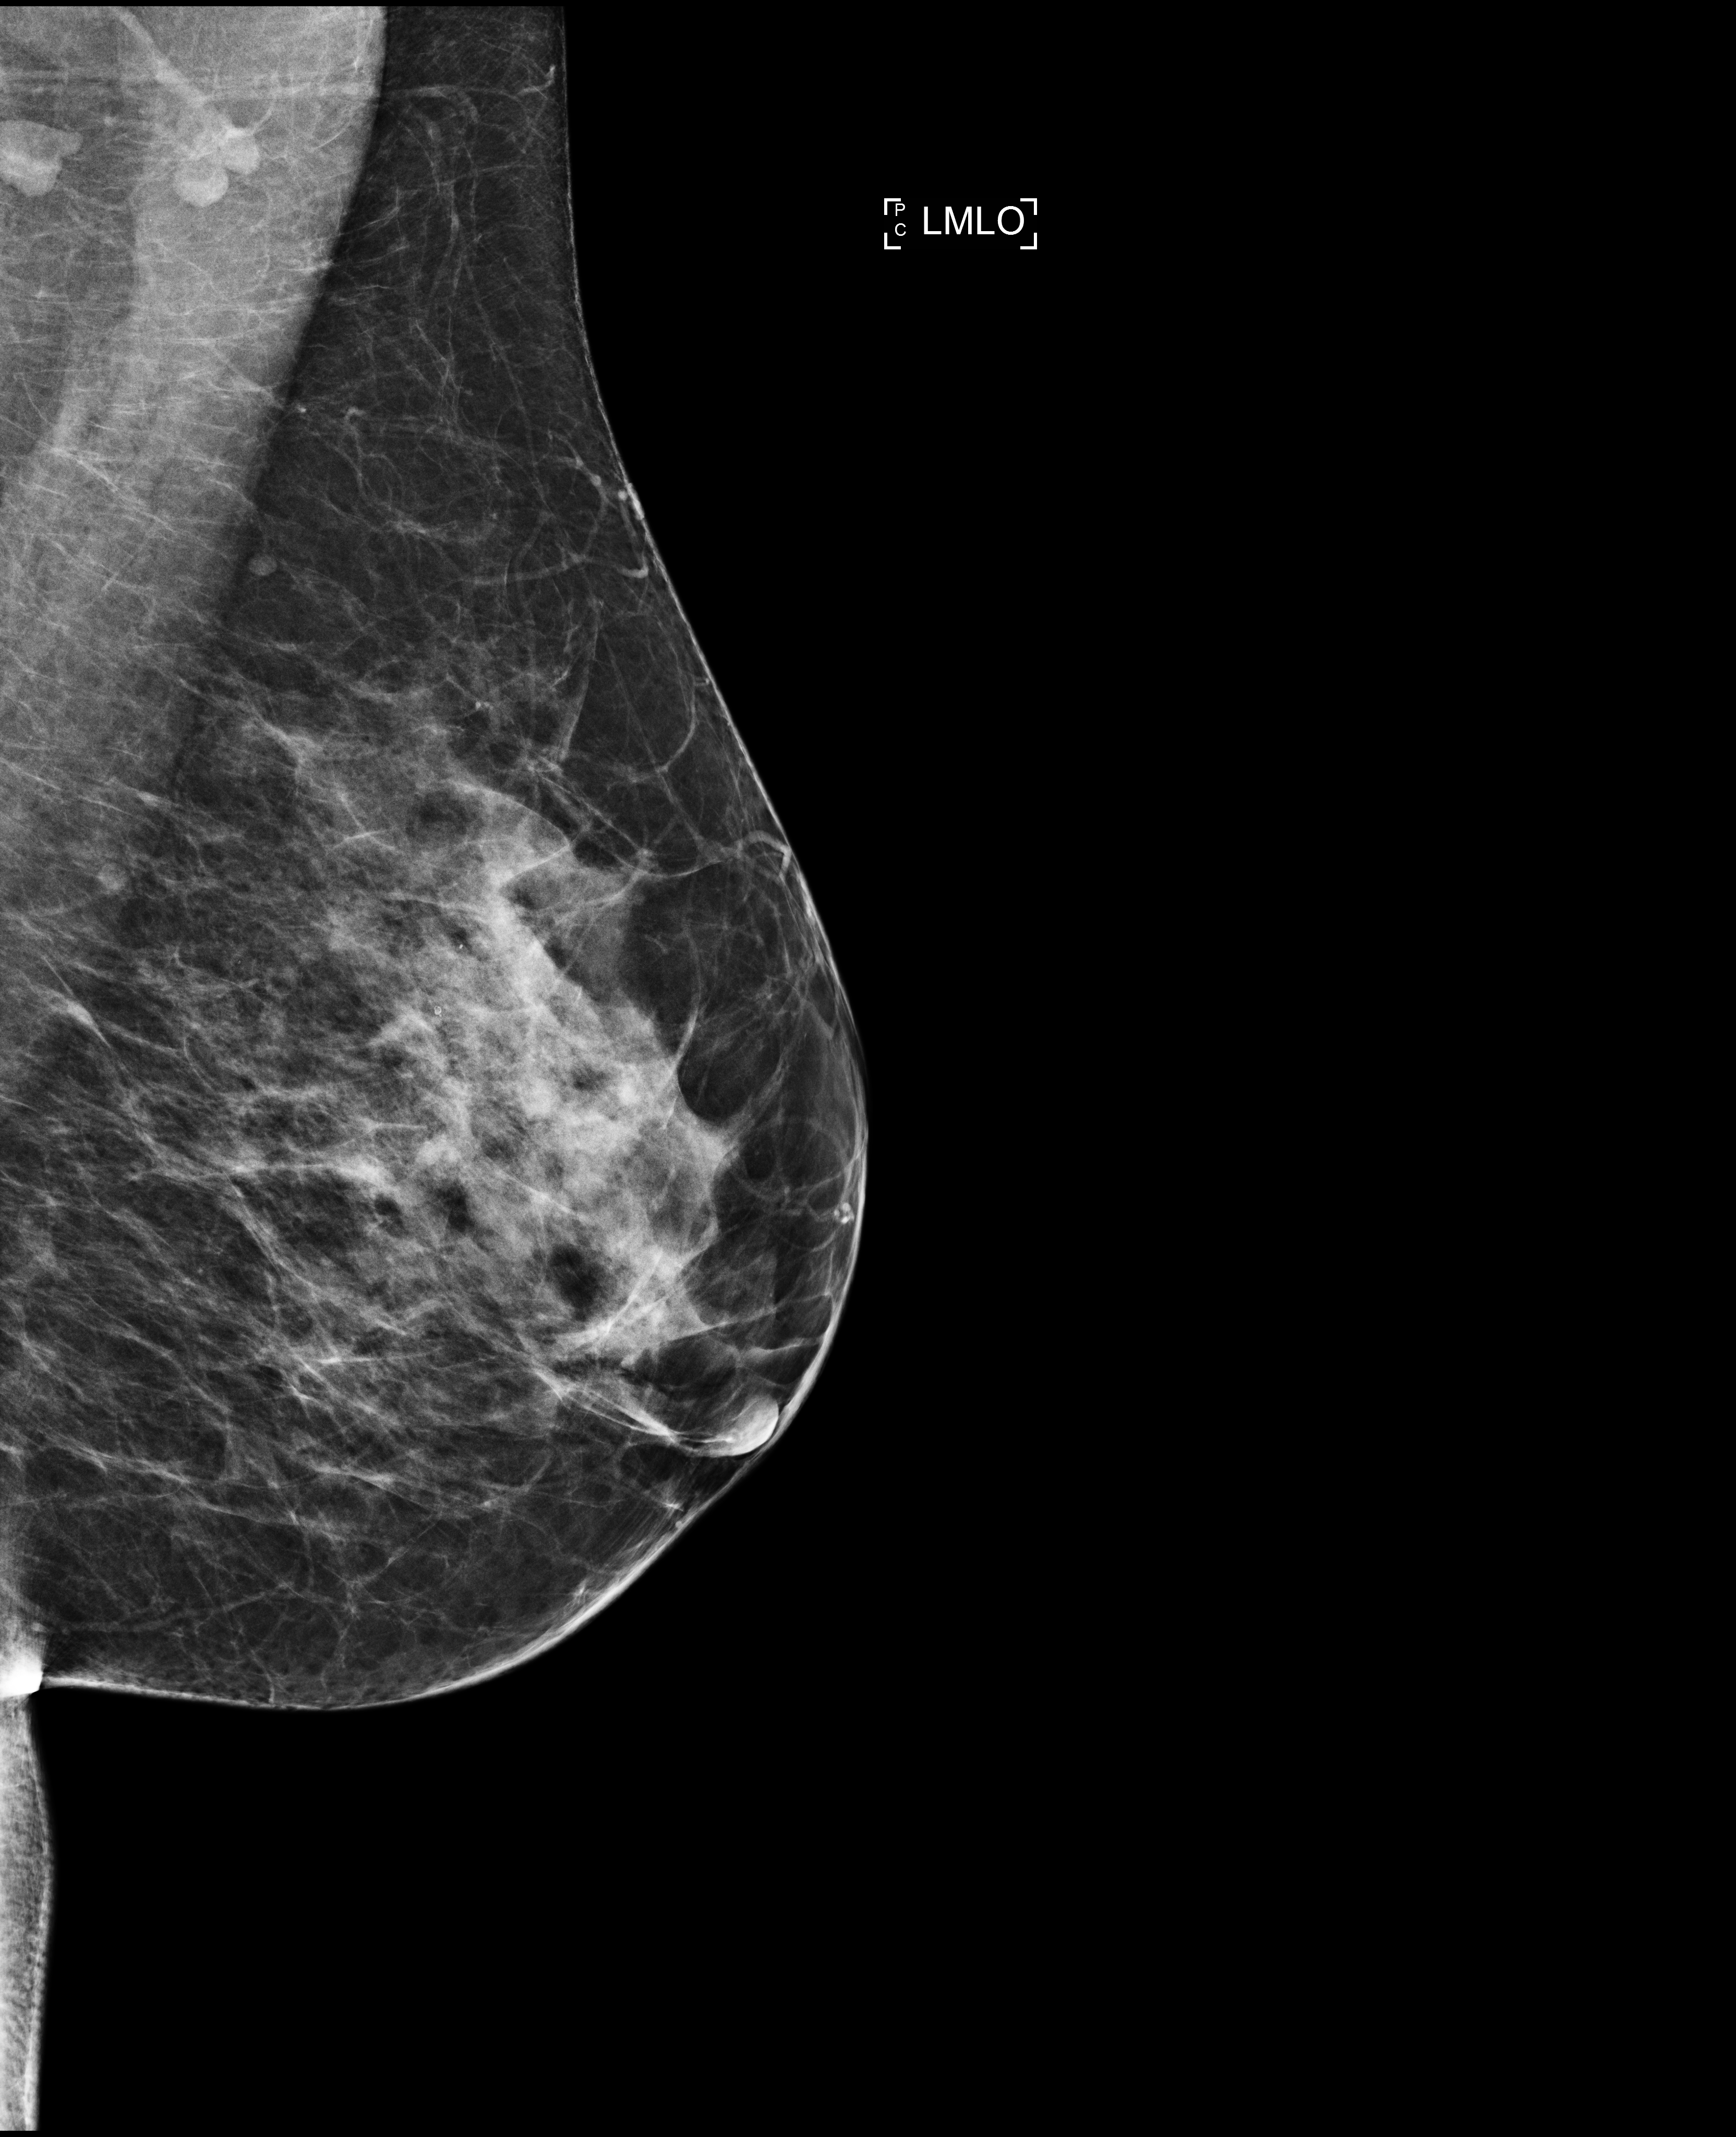
Annual screening mammography examination; compressed breast thickness 56 mm. Patient: female, 49 years.
Image type: full-field digital mammogram. Breast: left. Projection: medio-lateral oblique projection.